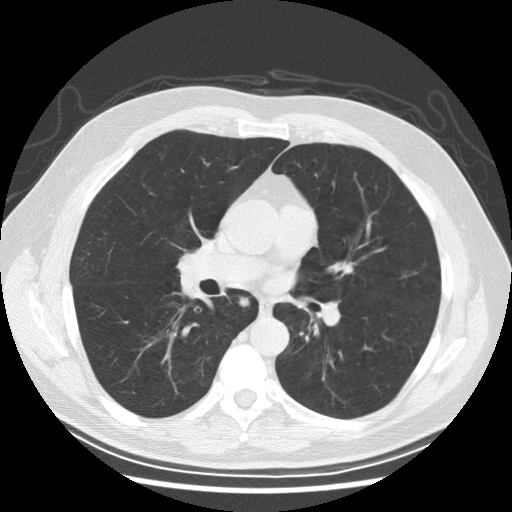
Chest CT (low-dose screening protocol), one axial image; second screening round (one year after baseline); lung window (W 1500 / L -600 HU); 120 kVp; slice 114 of 246 in the series. Male, age 61 years at enrolment. Former smoker at enrolment.
Expert-annotated lung lesion, box from (x=225, y=285) to (x=257, y=316) px. Screening reader's record for this exam: no non-calcified nodule ≥4 mm recorded. Later outcome: lung cancer diagnosed 382 days after this screen — squamous cell carcinoma, keratinizing, NOS, right lower lobe, stage IIIB (AJCC 6th edition), 40 mm at pathology.